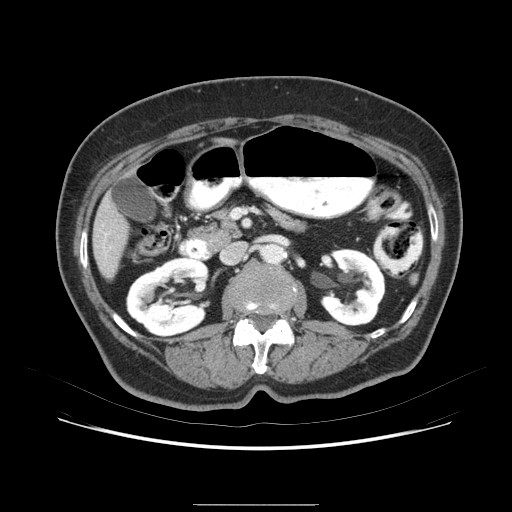
Contrast-enhanced abdominal CT (liver protocol), one axial slice; position 26 of 79 along the scan axis; 120 kVp; soft-tissue window (W 400 / L 40 HU); 2.5 mm slice thickness; 512 × 512 image matrix, field of view 380 × 380 mm. Case-level facts recorded for this patient, not image findings: diagnosis: hepatocellular carcinoma (patient treated with transarterial chemoembolisation; whether this scan precedes or follows treatment is not stated here); TNM stage (as recorded): Stage-I; Child-Pugh class: A; tumour differentiation: poorly differentiated.
Annotated regions visible in this slice (semi-automatically segmented with operator editing):
- liver parenchyma outside the tumour (the mass and vessels are separate outlines, so this box may not span the whole liver): bounding box [x1, y1, x2, y2] px = [90, 133, 254, 296]
- liver vessels: [113, 238, 132, 275]